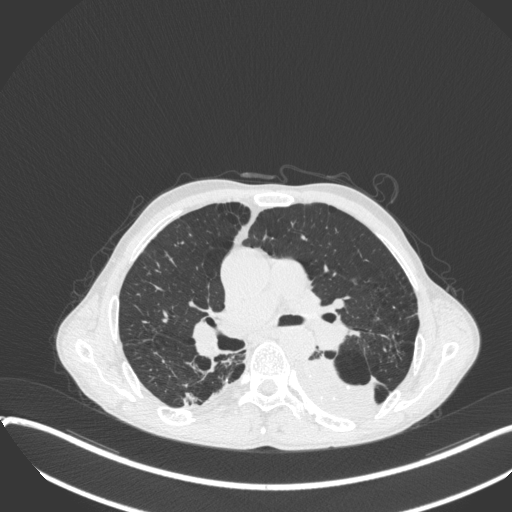
Chest CT, one axial slice; slice 226 of 400 in the series (ordered by position); lung window (W 1500 / L -600 HU); 512 × 512 image matrix, field of view 400 × 400 mm. Male patient, age 57 years. From the clinical record (not read from this slice): clinical TNM (as recorded): T4 N0 M0.
Structures marked on this image (rectangle marked by the reading radiologist):
- lung tumour (recorded histology: squamous cell carcinoma): bounding box <292,346,382,427> (left, top, right, bottom; pixels)